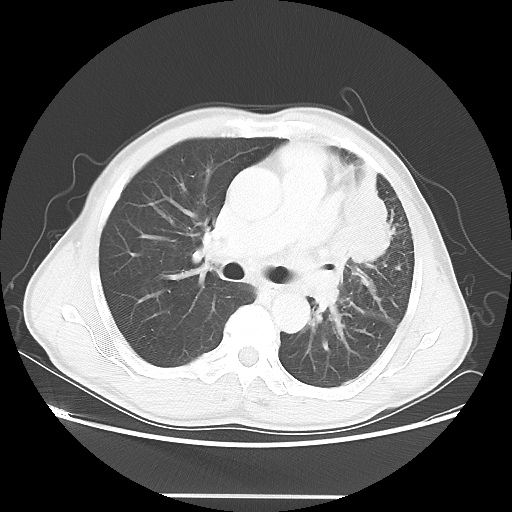
Chest CT, one axial slice. Slice 31 of 55 in the series (ordered by position). 100 kVp. Lung window (W 1500 / L -600 HU). 512 × 512 image matrix, field of view 398 × 398 mm. Patient: male, 60 years. From the clinical record (not read from this slice): clinical TNM (as recorded): T3 N3 M0.
Structures marked on this image (bounding box drawn by a radiologist):
- lung tumour (recorded histology: adenocarcinoma): bounding box [x1, y1, x2, y2] px = [343, 173, 392, 270]